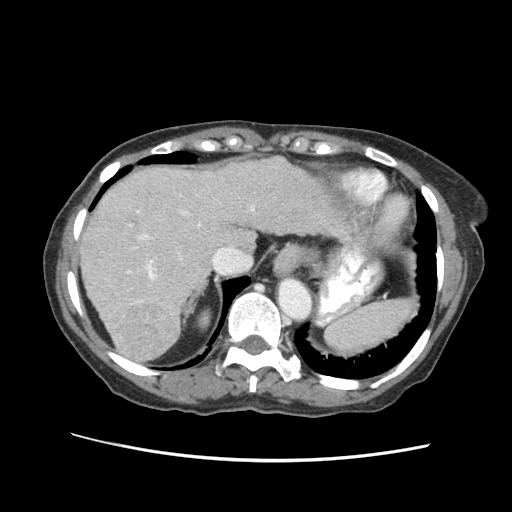
Contrast-enhanced abdominal CT (liver protocol), one axial slice; position 46 of 63 along the scan axis; soft-tissue window (W 400 / L 40 HU); 512 × 512 image matrix. From the clinical record (not read from this slice): diagnosis: hepatocellular carcinoma (patient treated with transarterial chemoembolisation; whether this scan precedes or follows treatment is not stated here); TNM stage (as recorded): Stage-I; Child-Pugh class: B.
Outlined on this slice (semi-automatically segmented with operator editing):
- liver parenchyma outside the tumour (the mass and vessels are separate outlines, so this box may not span the whole liver): bounding box <80,154,396,362> (left, top, right, bottom; pixels)
- mass: <114,299,177,360>
- liver vessels: <137,210,181,361>